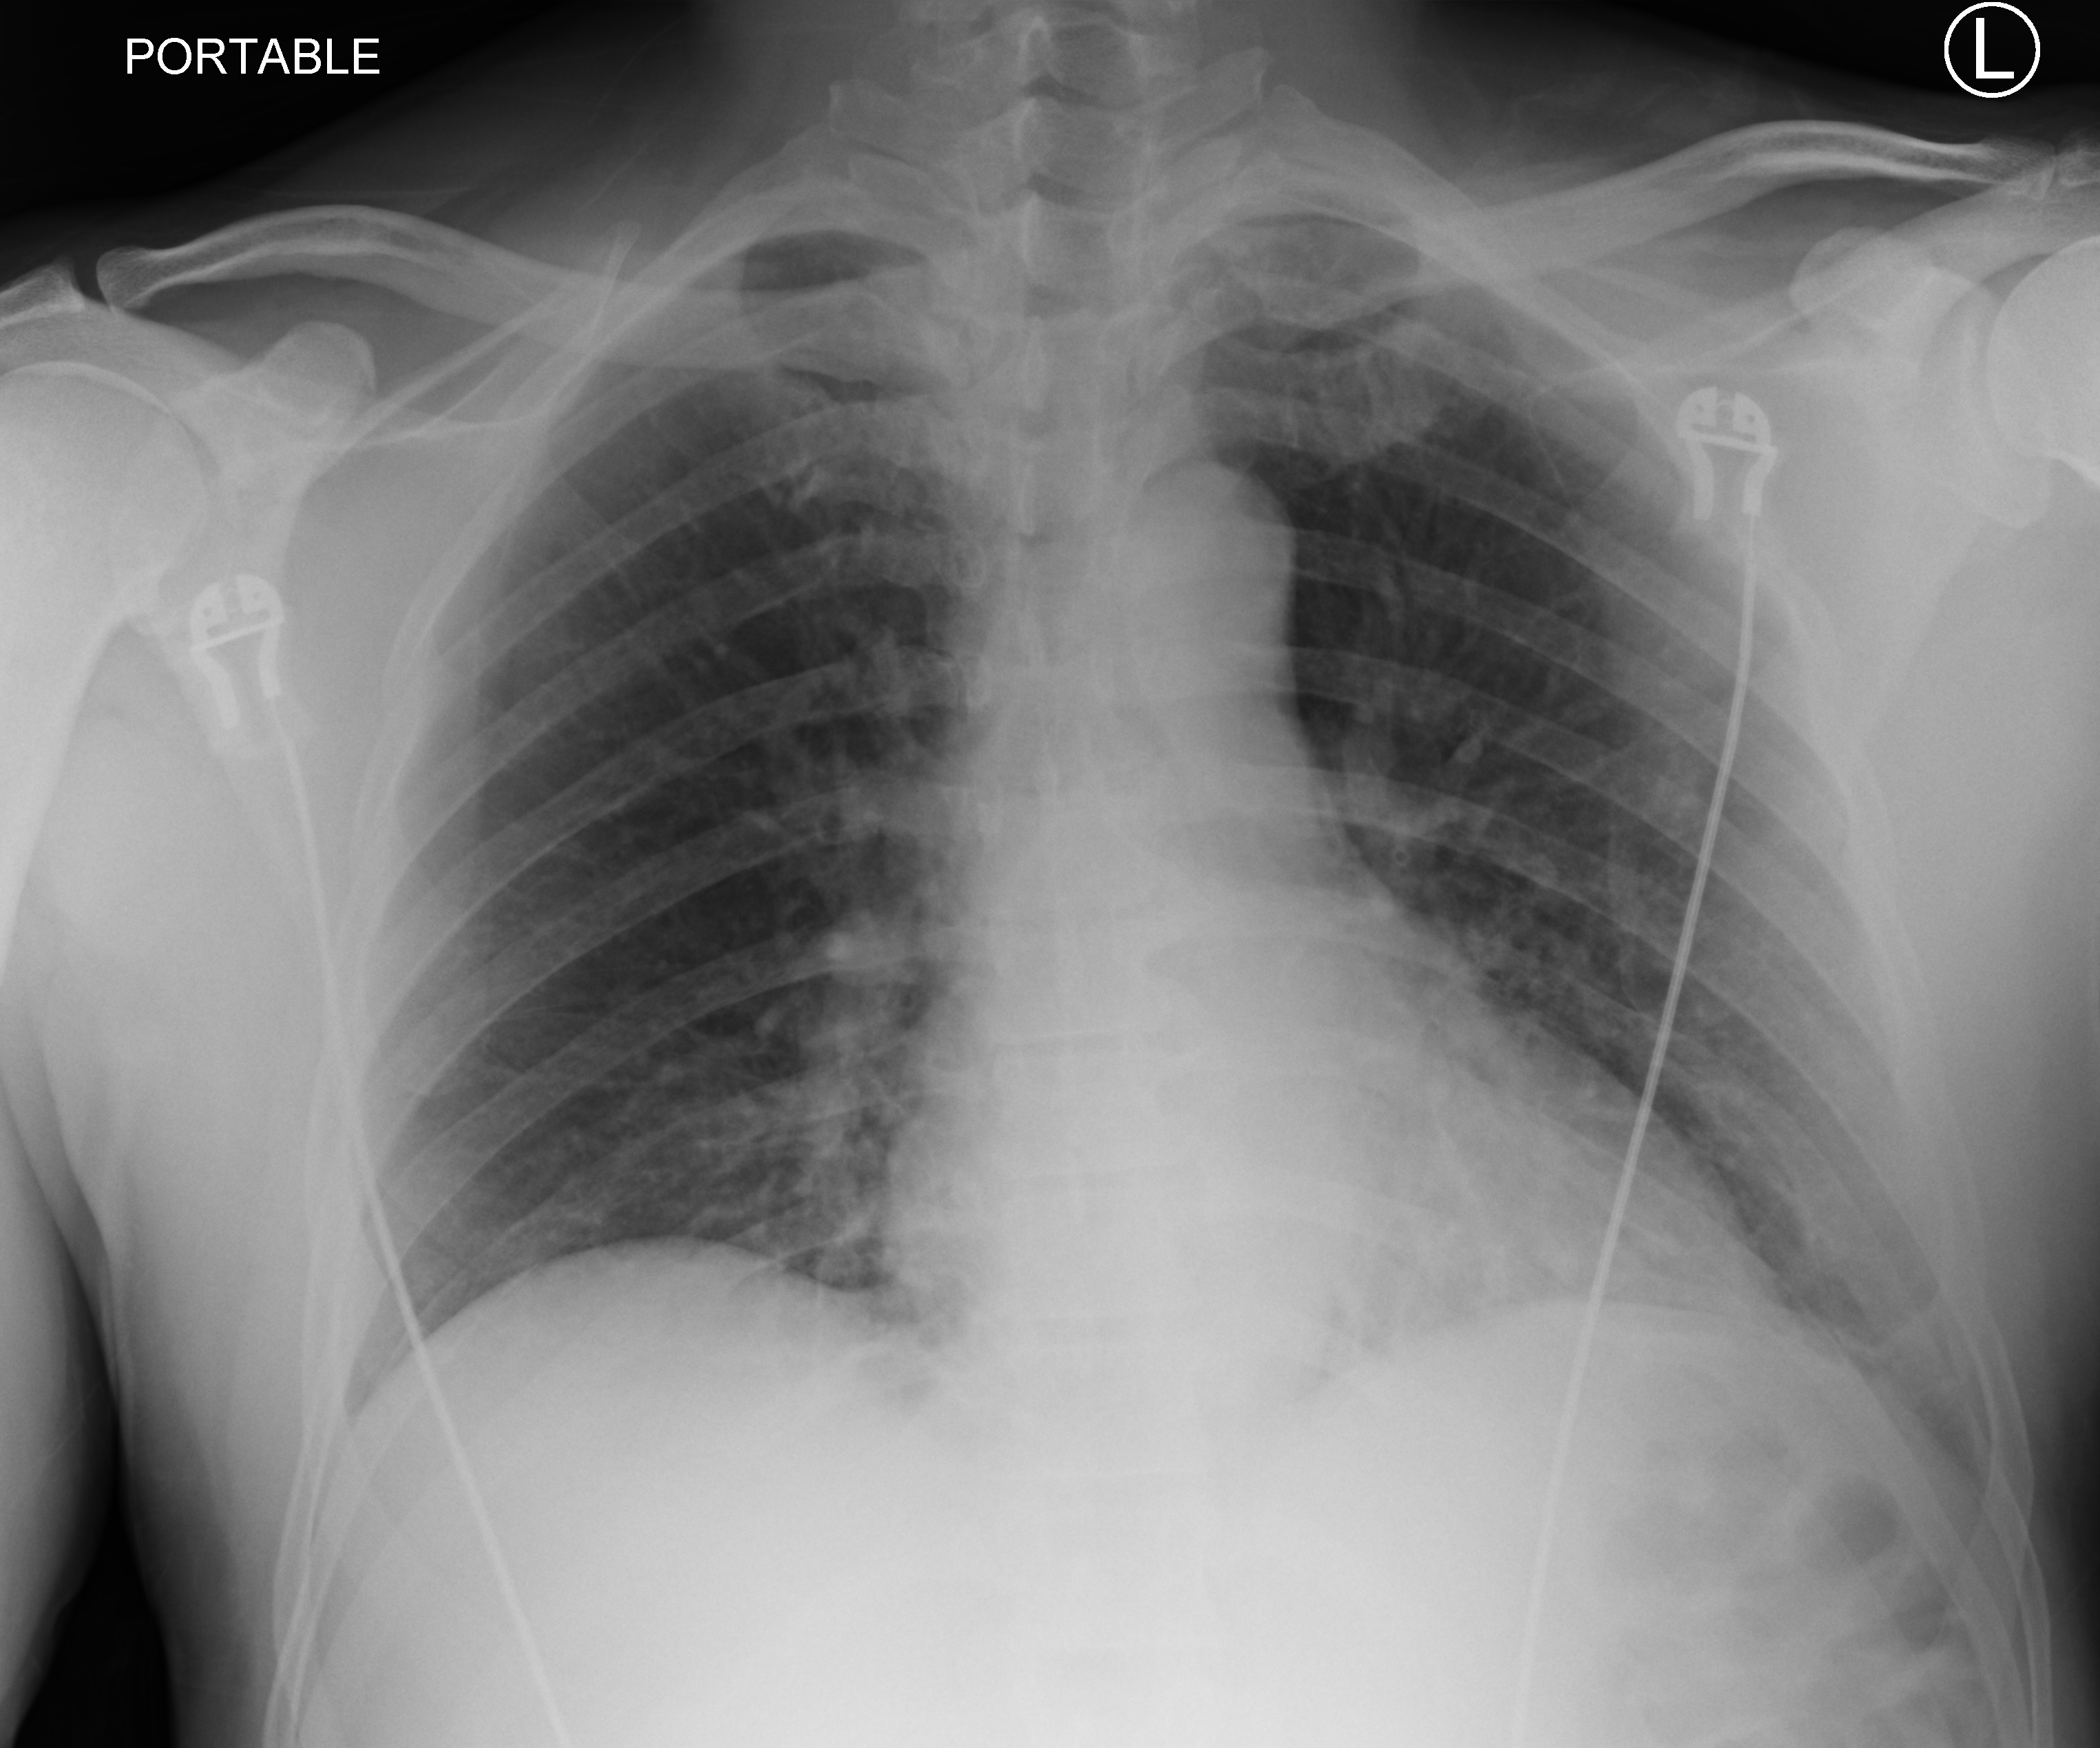
Bedside chest radiograph (computed radiography); anteroposterior (AP) projection. Patient hospitalised with COVID-19; male, aged 18–59 years.
Hospital-stay facts (about this admission, not read from this image; timing relative to this image not recorded): admitted to intensive care during this hospital stay: no; mechanically ventilated during this hospital stay: no.